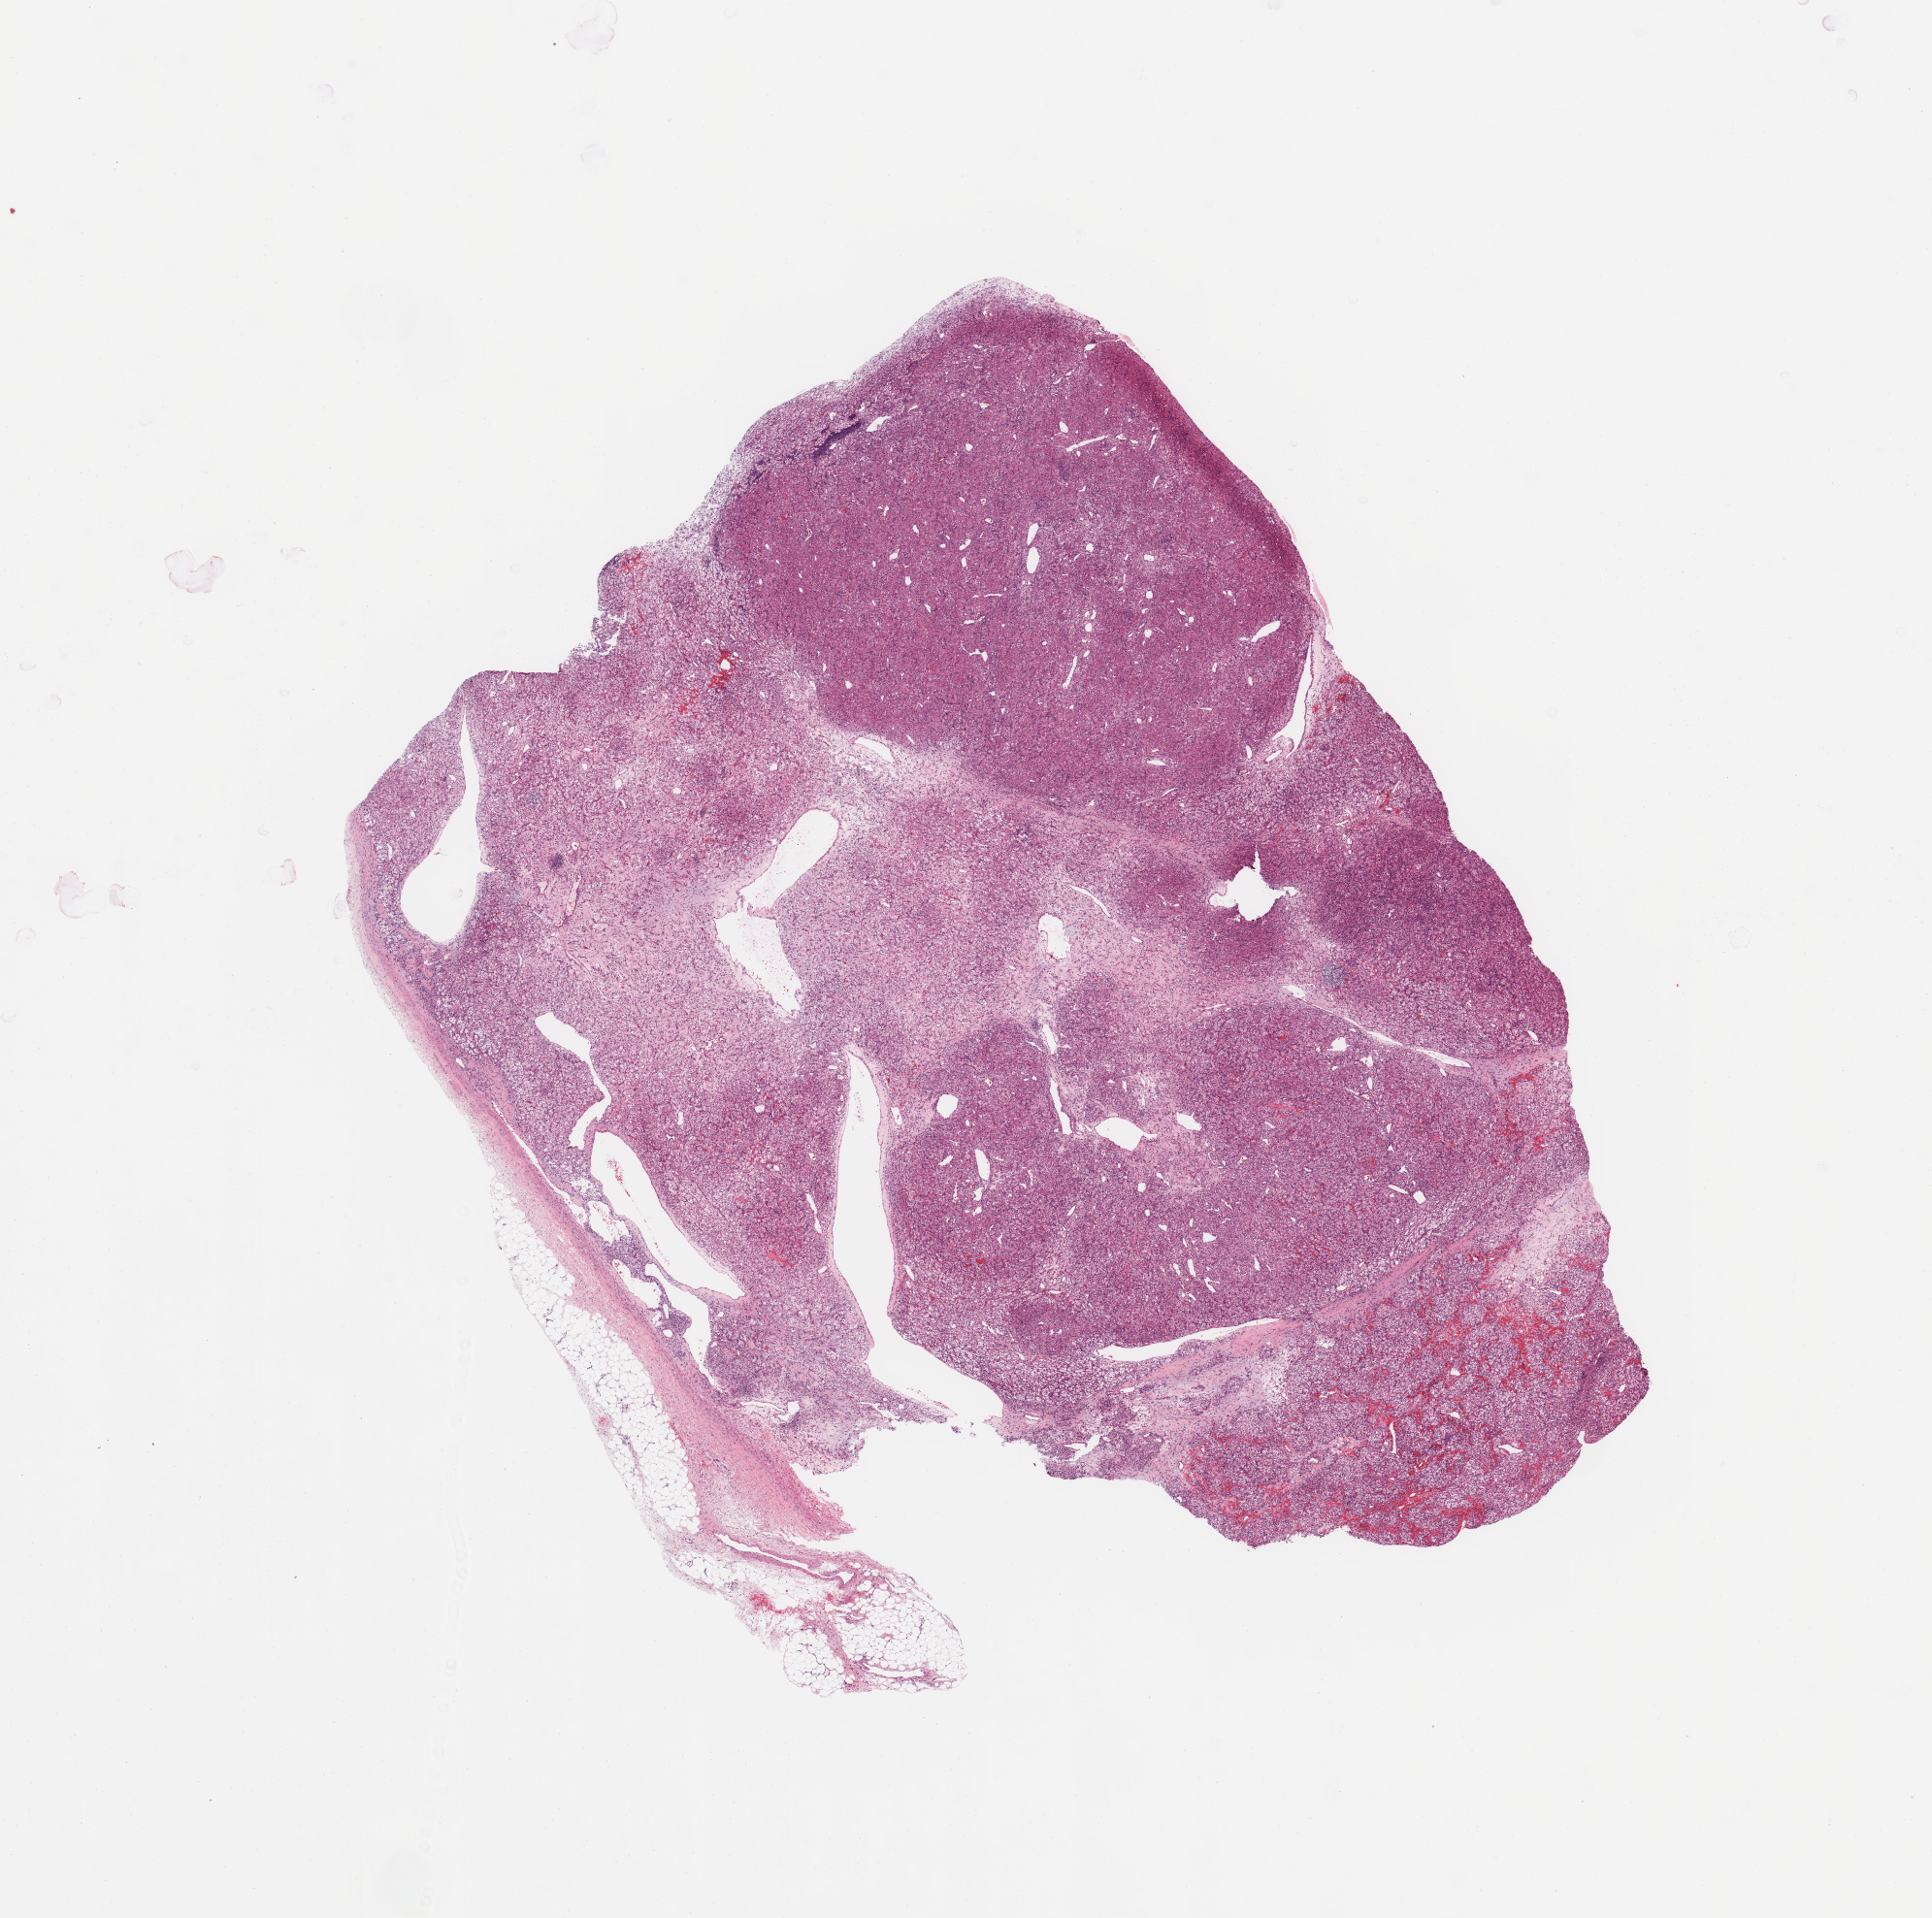
Whole-slide histology image, H&E-stained, shown as a low-resolution overview of the whole scanned area (about 15.8 x 15.6 mm, acquisition: 20x scan). Tumour tissue sample, sampled site: kidney. Male, 47 y/o. Histologic grade: G3 (poorly differentiated). Composition of this section per pathologist review: tumour nuclei 80%, necrosis 2%.
• AJCC pathologic stage: I
• diagnosis: Renal cell carcinoma, NOS
• primary tumour site (as recorded): upper pole